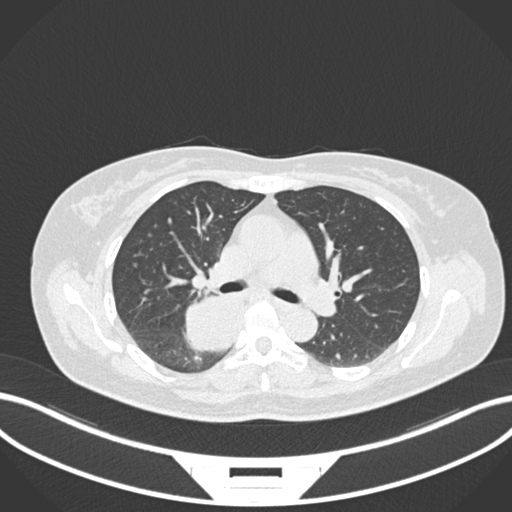
Chest CT, one axial slice; slice 614 of 677 in the series (ordered by position); lung window (W 1500 / L -600 HU); 512 × 512 image matrix. Patient: female, 54 years. Case-level facts recorded for this patient, not image findings: clinical TNM (as recorded): T4 N0 M0.
Structures marked on this image (rectangle marked by the reading radiologist):
- lung tumour (recorded histology: adenocarcinoma): bounding box <181,282,251,358> (left, top, right, bottom; pixels)